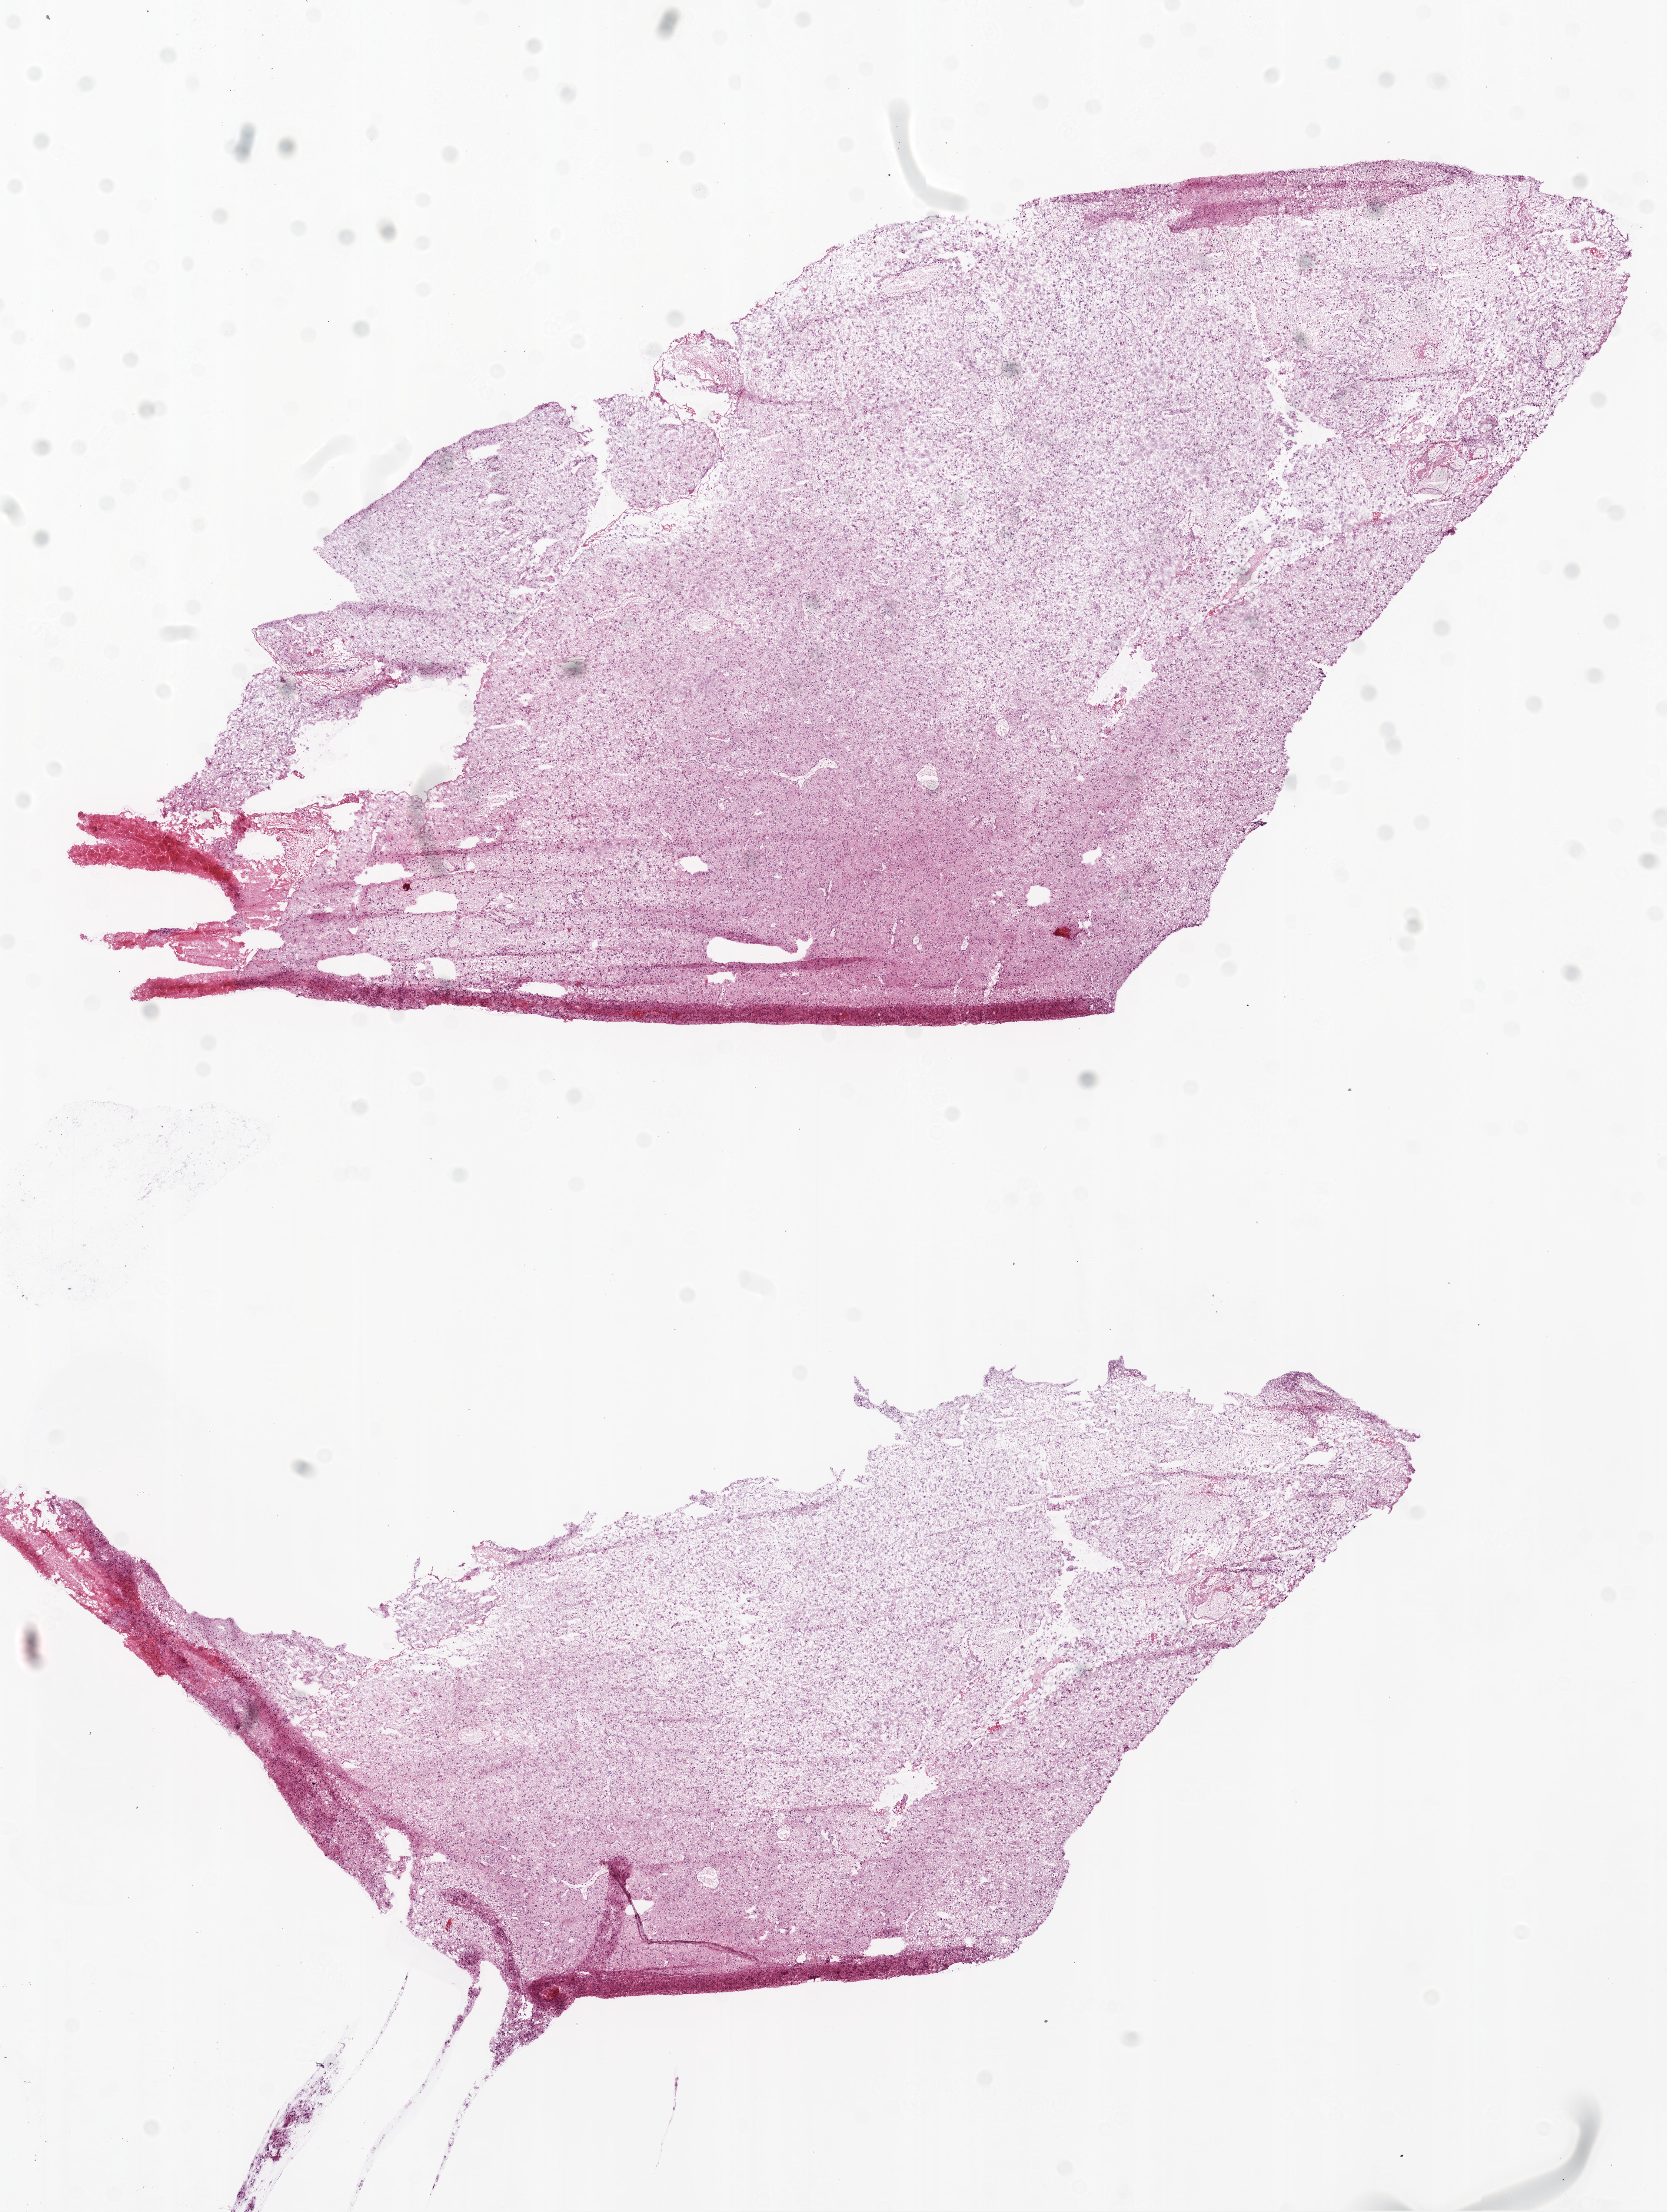
H&E-stained whole-slide image, a low-resolution overview of the entire scanned area, about 9.0 x 12.0 mm (slide scanned at 20x). Frozen section from the top of the tissue portion. Primary tumour sample from the brain. Patient: female, age at initial diagnosis 69 years. Pathologist review of this section (percent, as recorded): tumour cells 95%, tumour nuclei 60%.
Pathologic diagnosis: Glioblastoma.